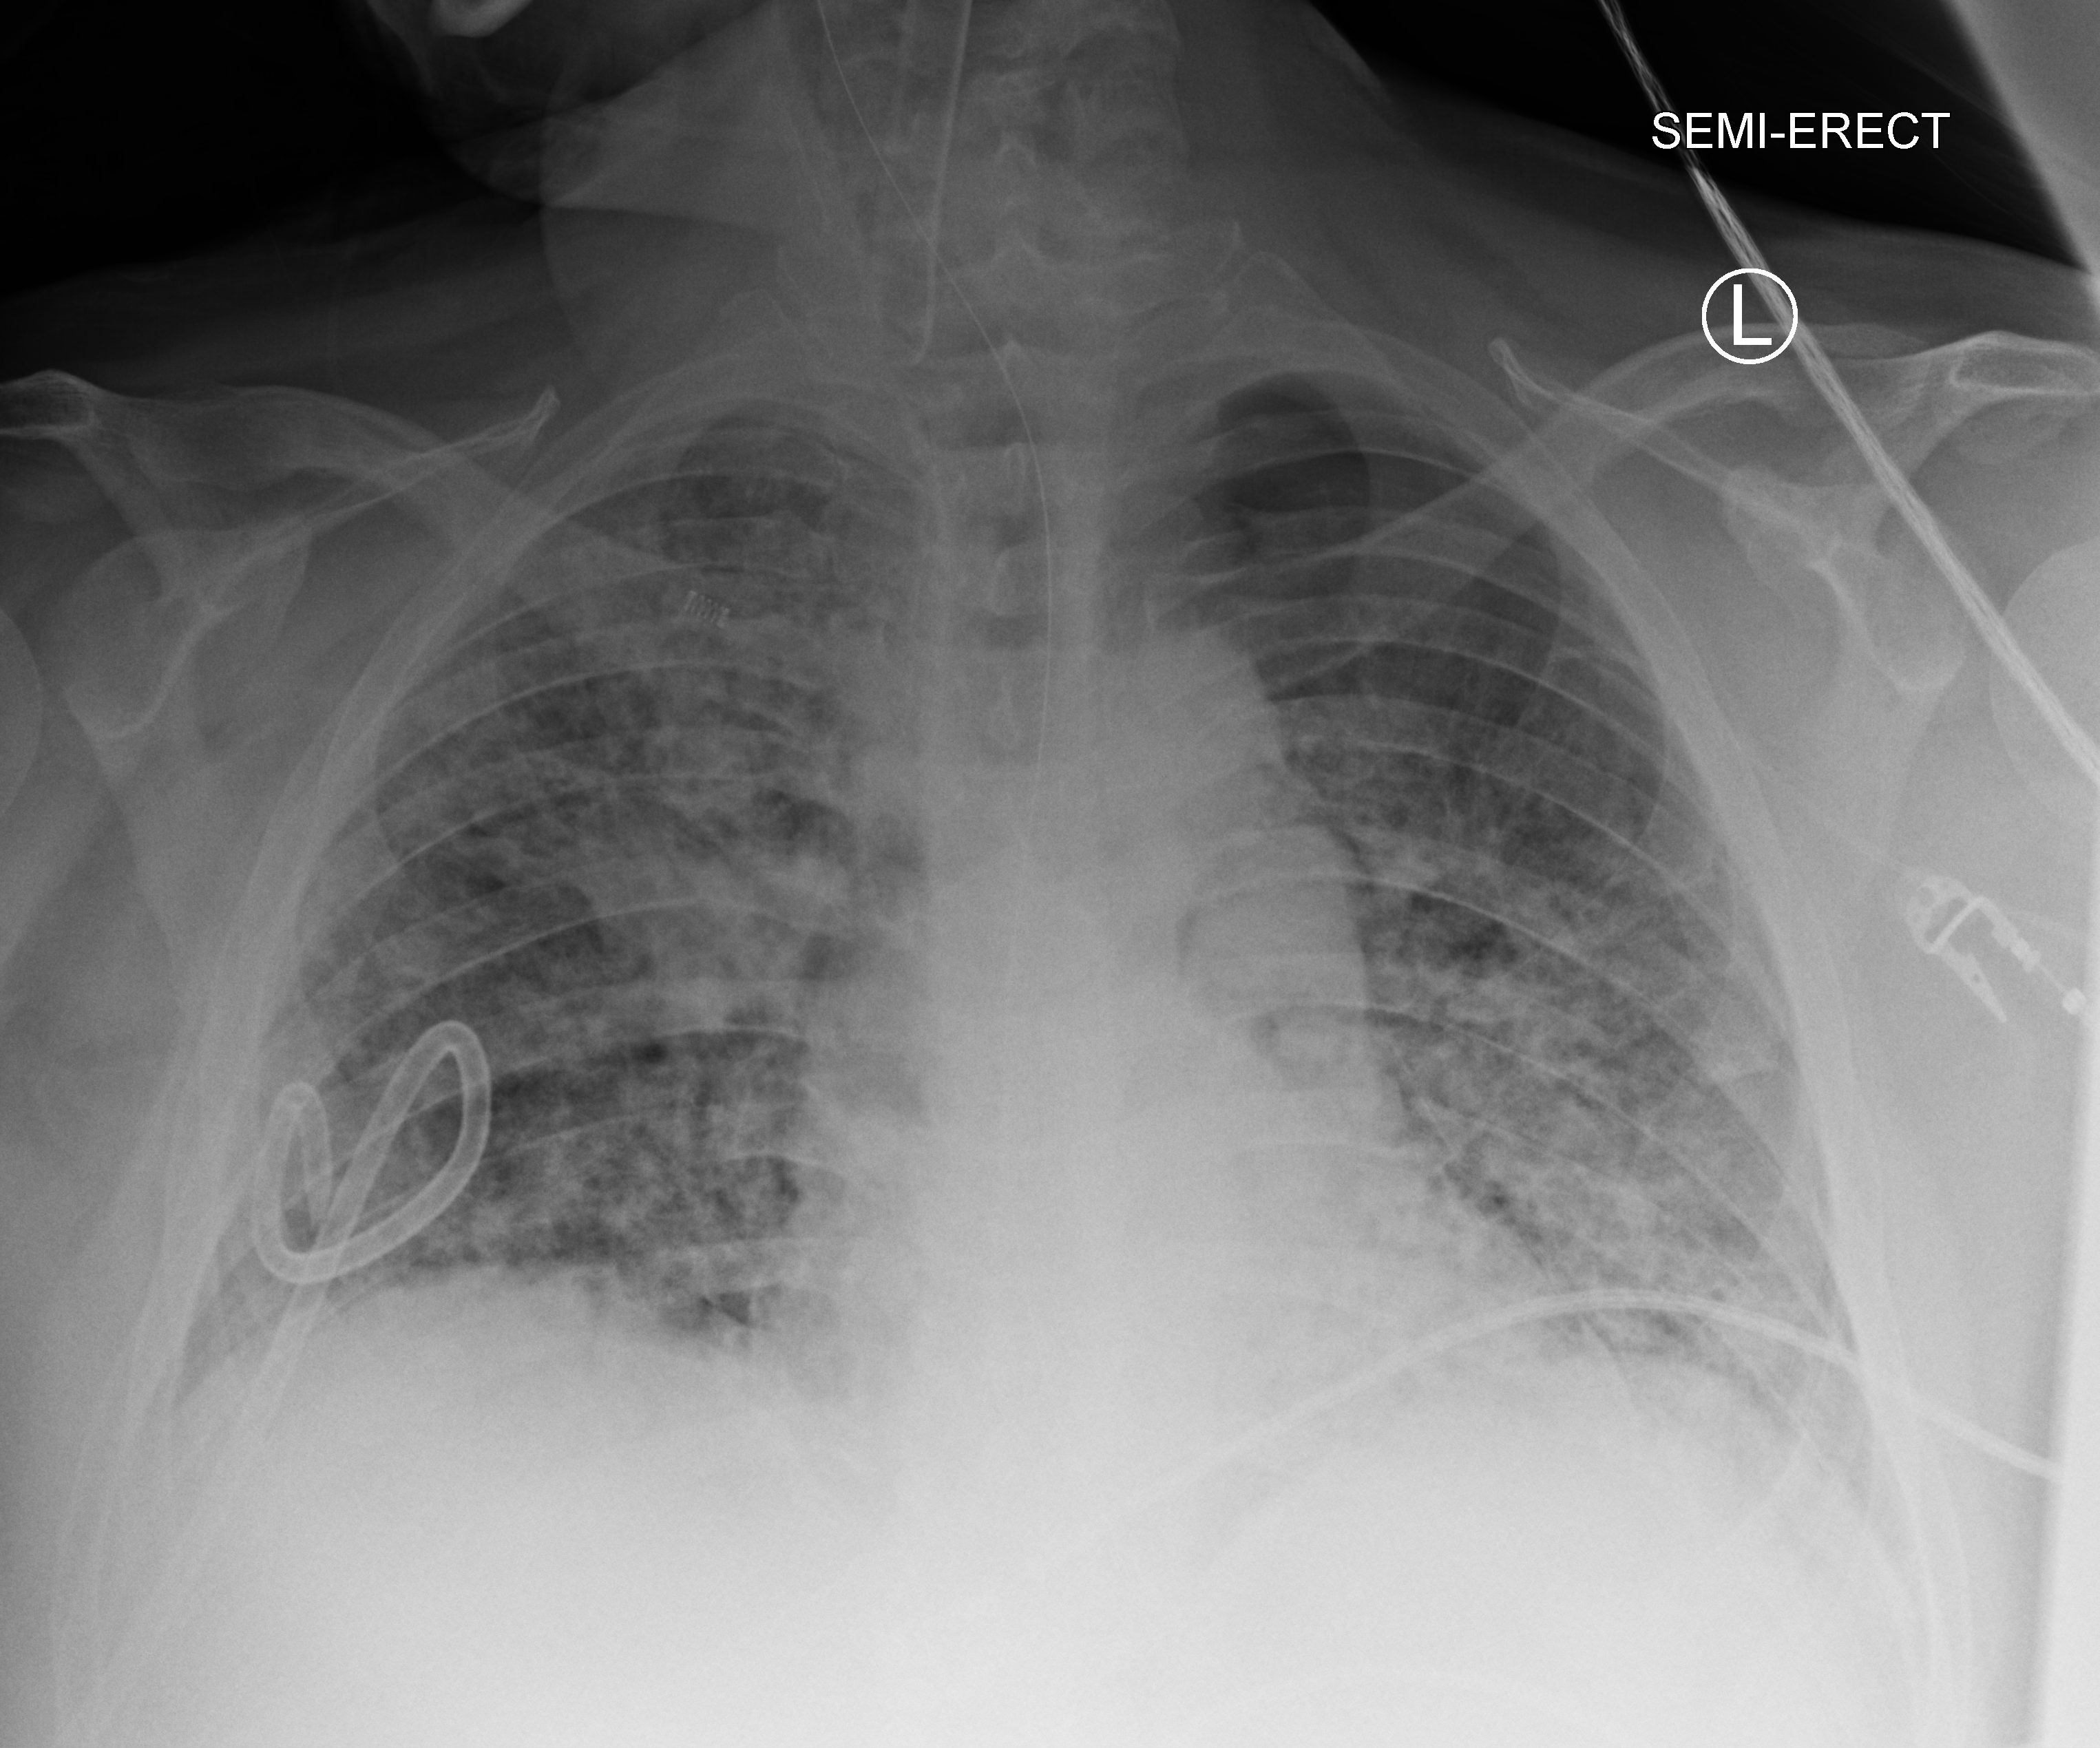
Bedside chest radiograph (computed radiography), anteroposterior (AP) projection. Patient hospitalised with COVID-19, aged 18–59 years.
Hospital-stay facts (about this admission, not read from this image; timing relative to this image not recorded): mechanically ventilated during this hospital stay: yes; admitted to intensive care during this hospital stay: yes.